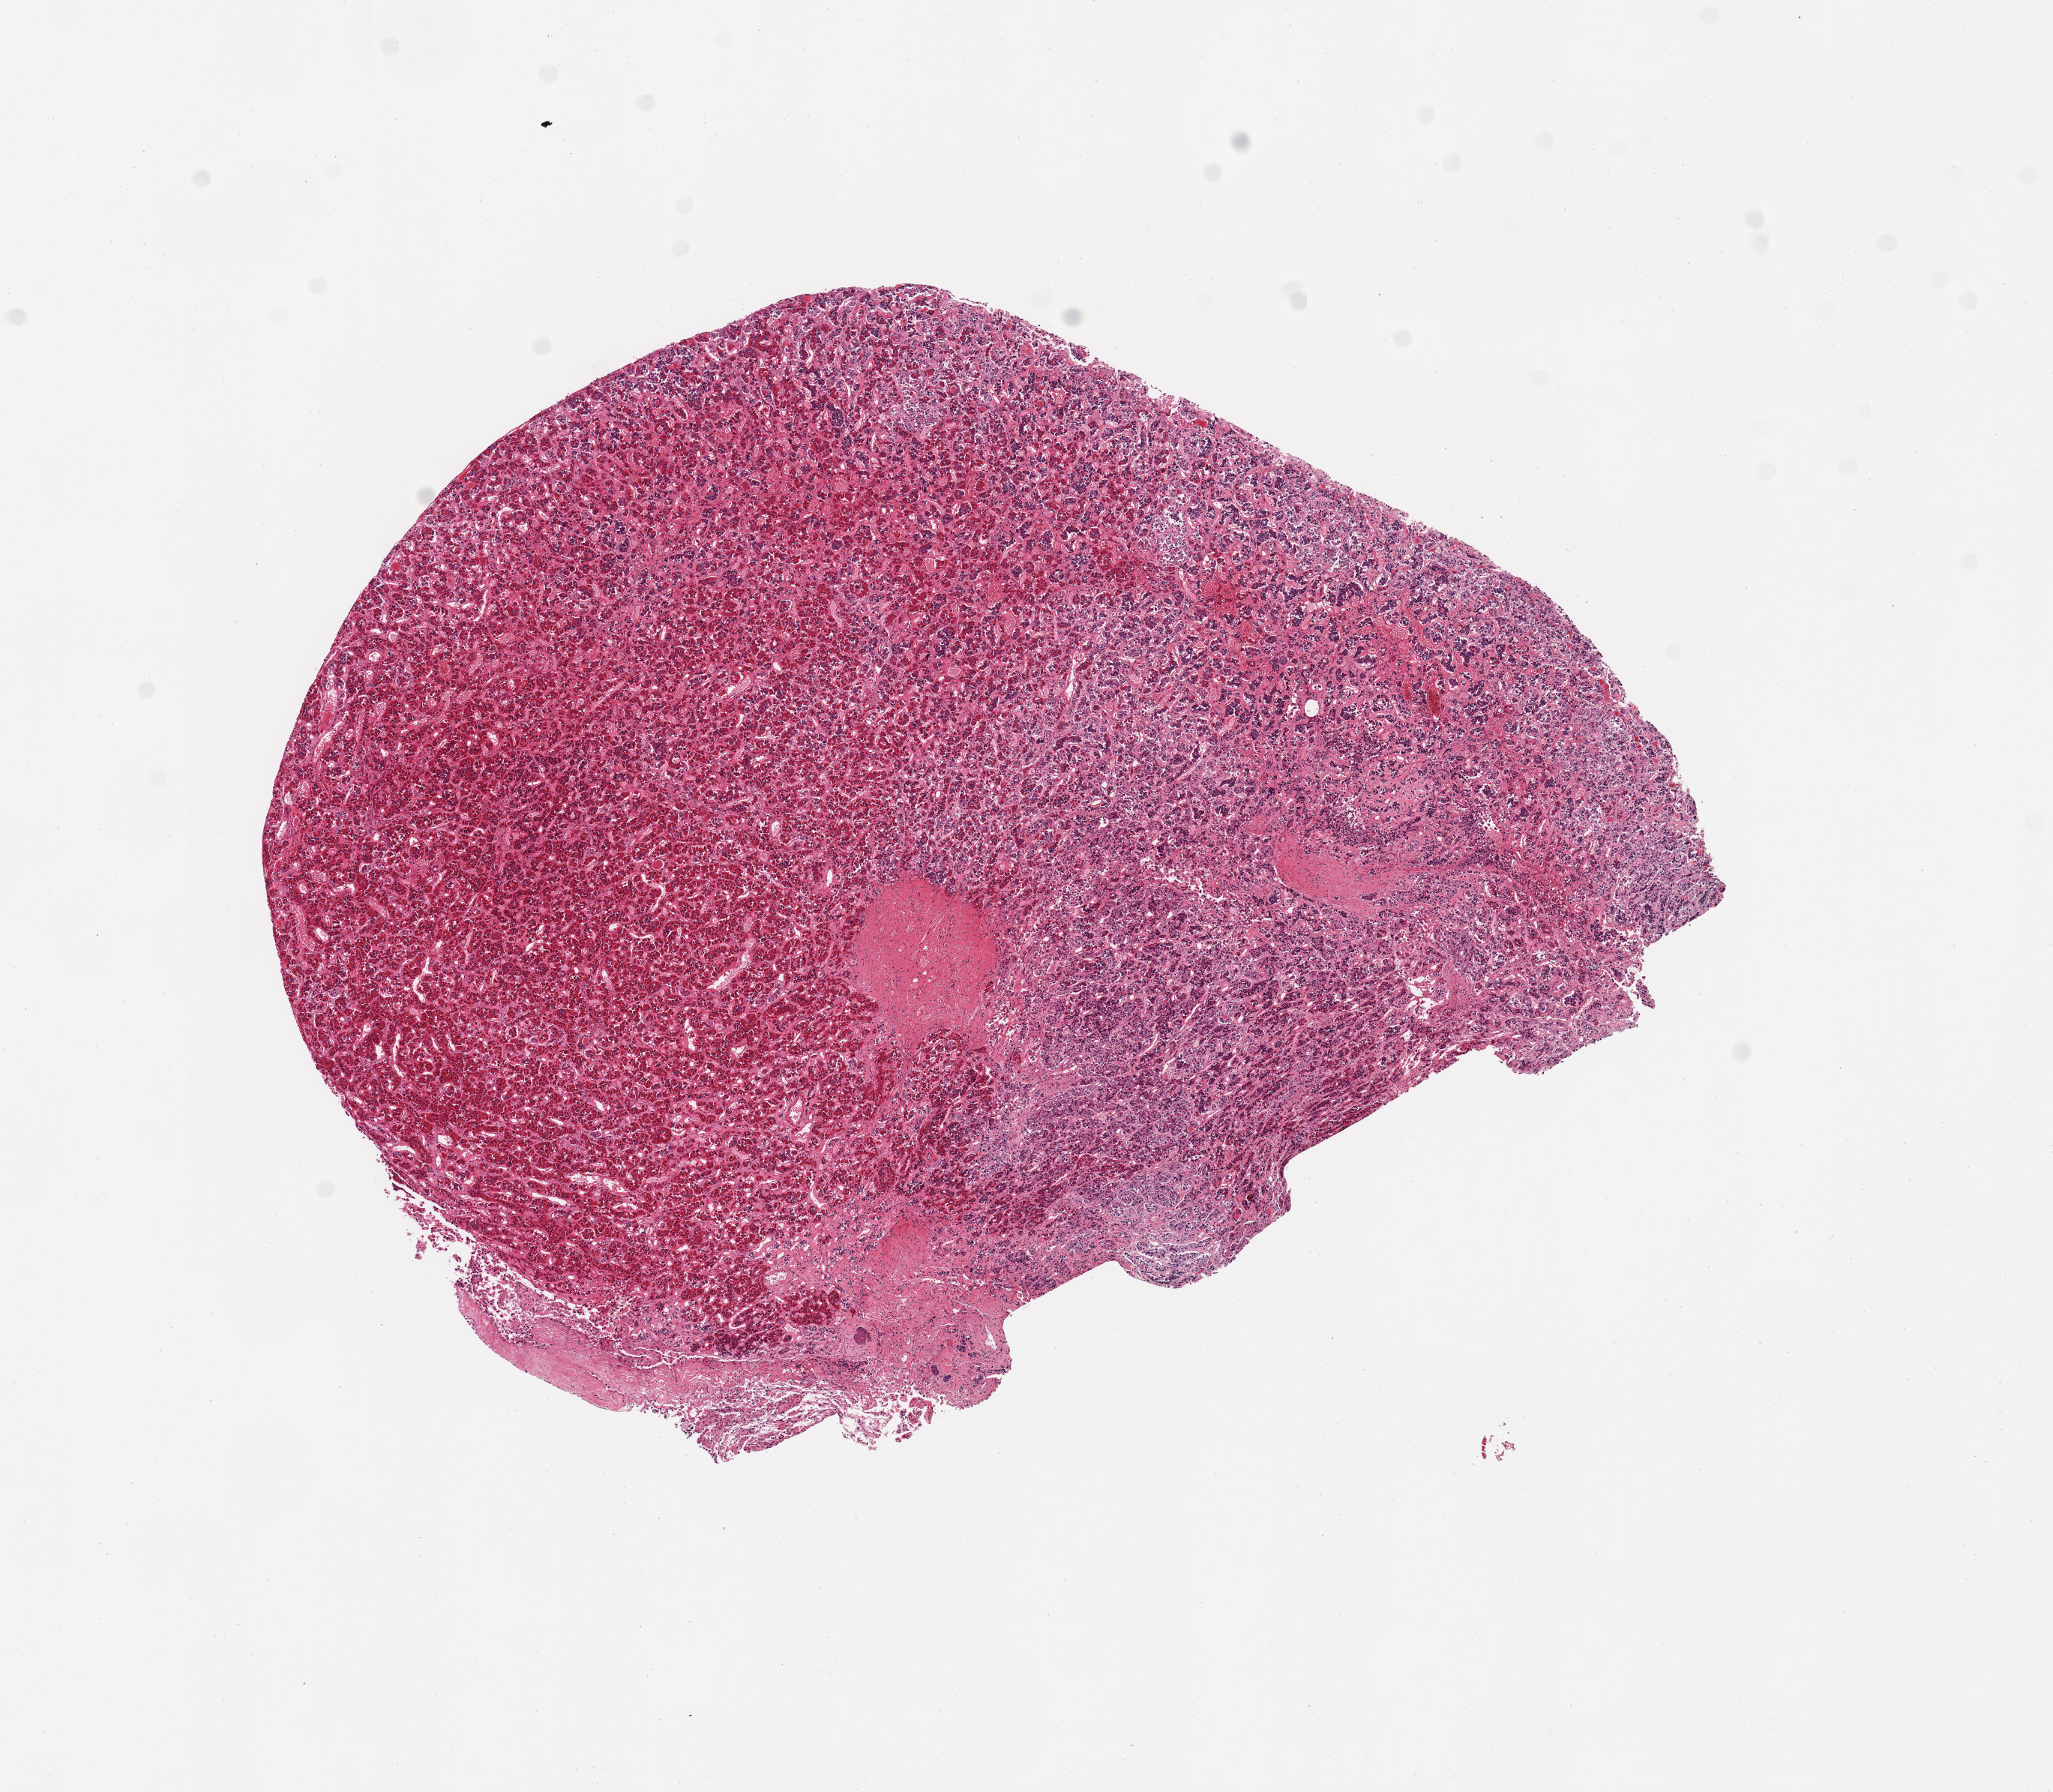
Whole-slide image, haematoxylin and eosin stain — whole scanned area (about 10.8 x 9.5 mm) shown as a low-resolution overview, PAXgene-fixed, paraffin-embedded tissue, section of pituitary (target tissue), tissue donor sample.
Pathologist's review note for this sample: 1 piece; adenohypophysis.